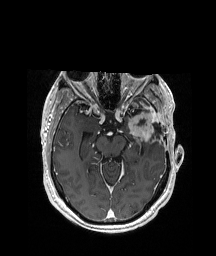
Brain MRI from a brain-tumour surgery series, one axial slice; T1-weighted post-contrast; 1 mm slice thickness; 216 × 256 image matrix. Case-level facts recorded for this patient, not image findings: histopathology: Glioblastoma; WHO grade: 4; IDH mutation: no; tumour location: Left Anterior/Superior Temporal.
Outlined on this slice (manually delineated by an expert):
- previous resection cavity: bounding box <137,119,161,134> (left, top, right, bottom; pixels)
- tumour: <123,108,158,141>